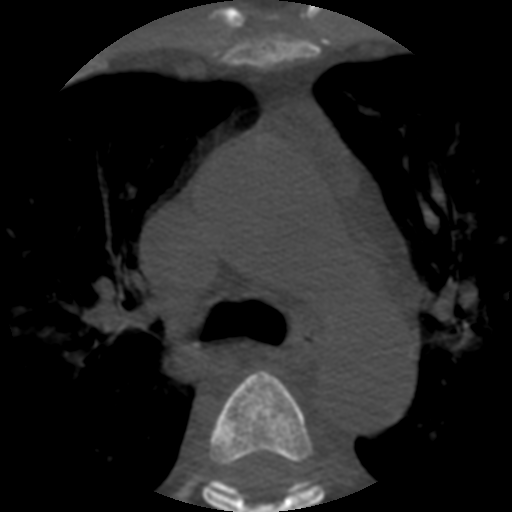
CT including the spine, one axial slice; slice 391 of 508 in the series (ordered by position); reconstruction kernel STANDARD; bone window (W 1800 / L 400 HU); 512 × 512 image matrix. Patient age 57 years. From the clinical record (not read from this slice): primary cancer: prostate.
Outlined on this slice (semi-automatic segmentation, software-assisted and operator-edited):
- T4 vertebra: box from (x=202, y=371) to (x=325, y=512) px
- T5 vertebra: (x=208, y=479)–(x=314, y=496)